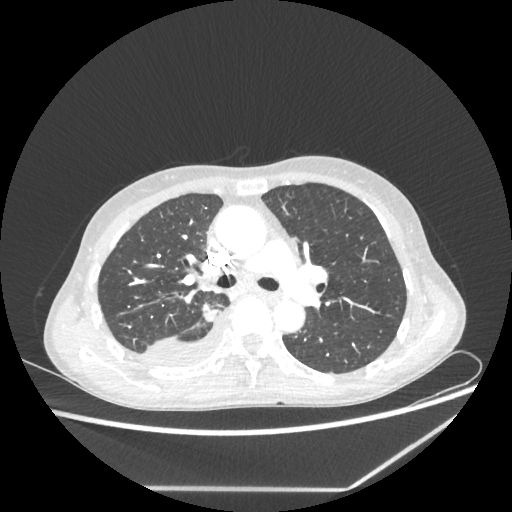
Chest CT, one axial slice. Position 147 of 237 along the scan axis. Reconstruction kernel STANDARD. Lung window (W 1500 / L -600 HU). 1.25 mm slice thickness. 512 × 512 image matrix. Patient: female, 59 years. Case-level facts recorded for this patient, not image findings: clinical TNM (as recorded): T1c N1 M1.
Structures marked on this image (bounding box drawn by a radiologist):
- lung tumour (recorded histology: adenocarcinoma): bounding box (x1, y1, x2, y2) in pixels: (201, 306, 219, 324)